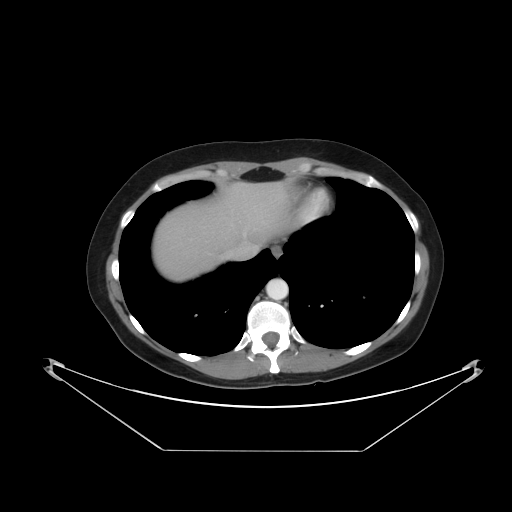
Contrast-enhanced abdominal CT, one axial slice; reconstruction kernel STANDARD; soft-tissue window (W 400 / L 40 HU); 512 × 512 image matrix, field of view 482 × 482 mm. Female patient, age 38 years. From the clinical record (not read from this slice): diagnosis: colorectal cancer liver metastases, imaged before liver resection; multiple liver metastases: yes.
Outlined on this slice (manually delineated by an expert):
- hepatic veins: bounding box (x1, y1, x2, y2) in pixels: (244, 222, 265, 235)
- liver: (152, 182, 290, 282)
- planned liver remnant (the part of the liver to remain after resection): (217, 182, 291, 245)